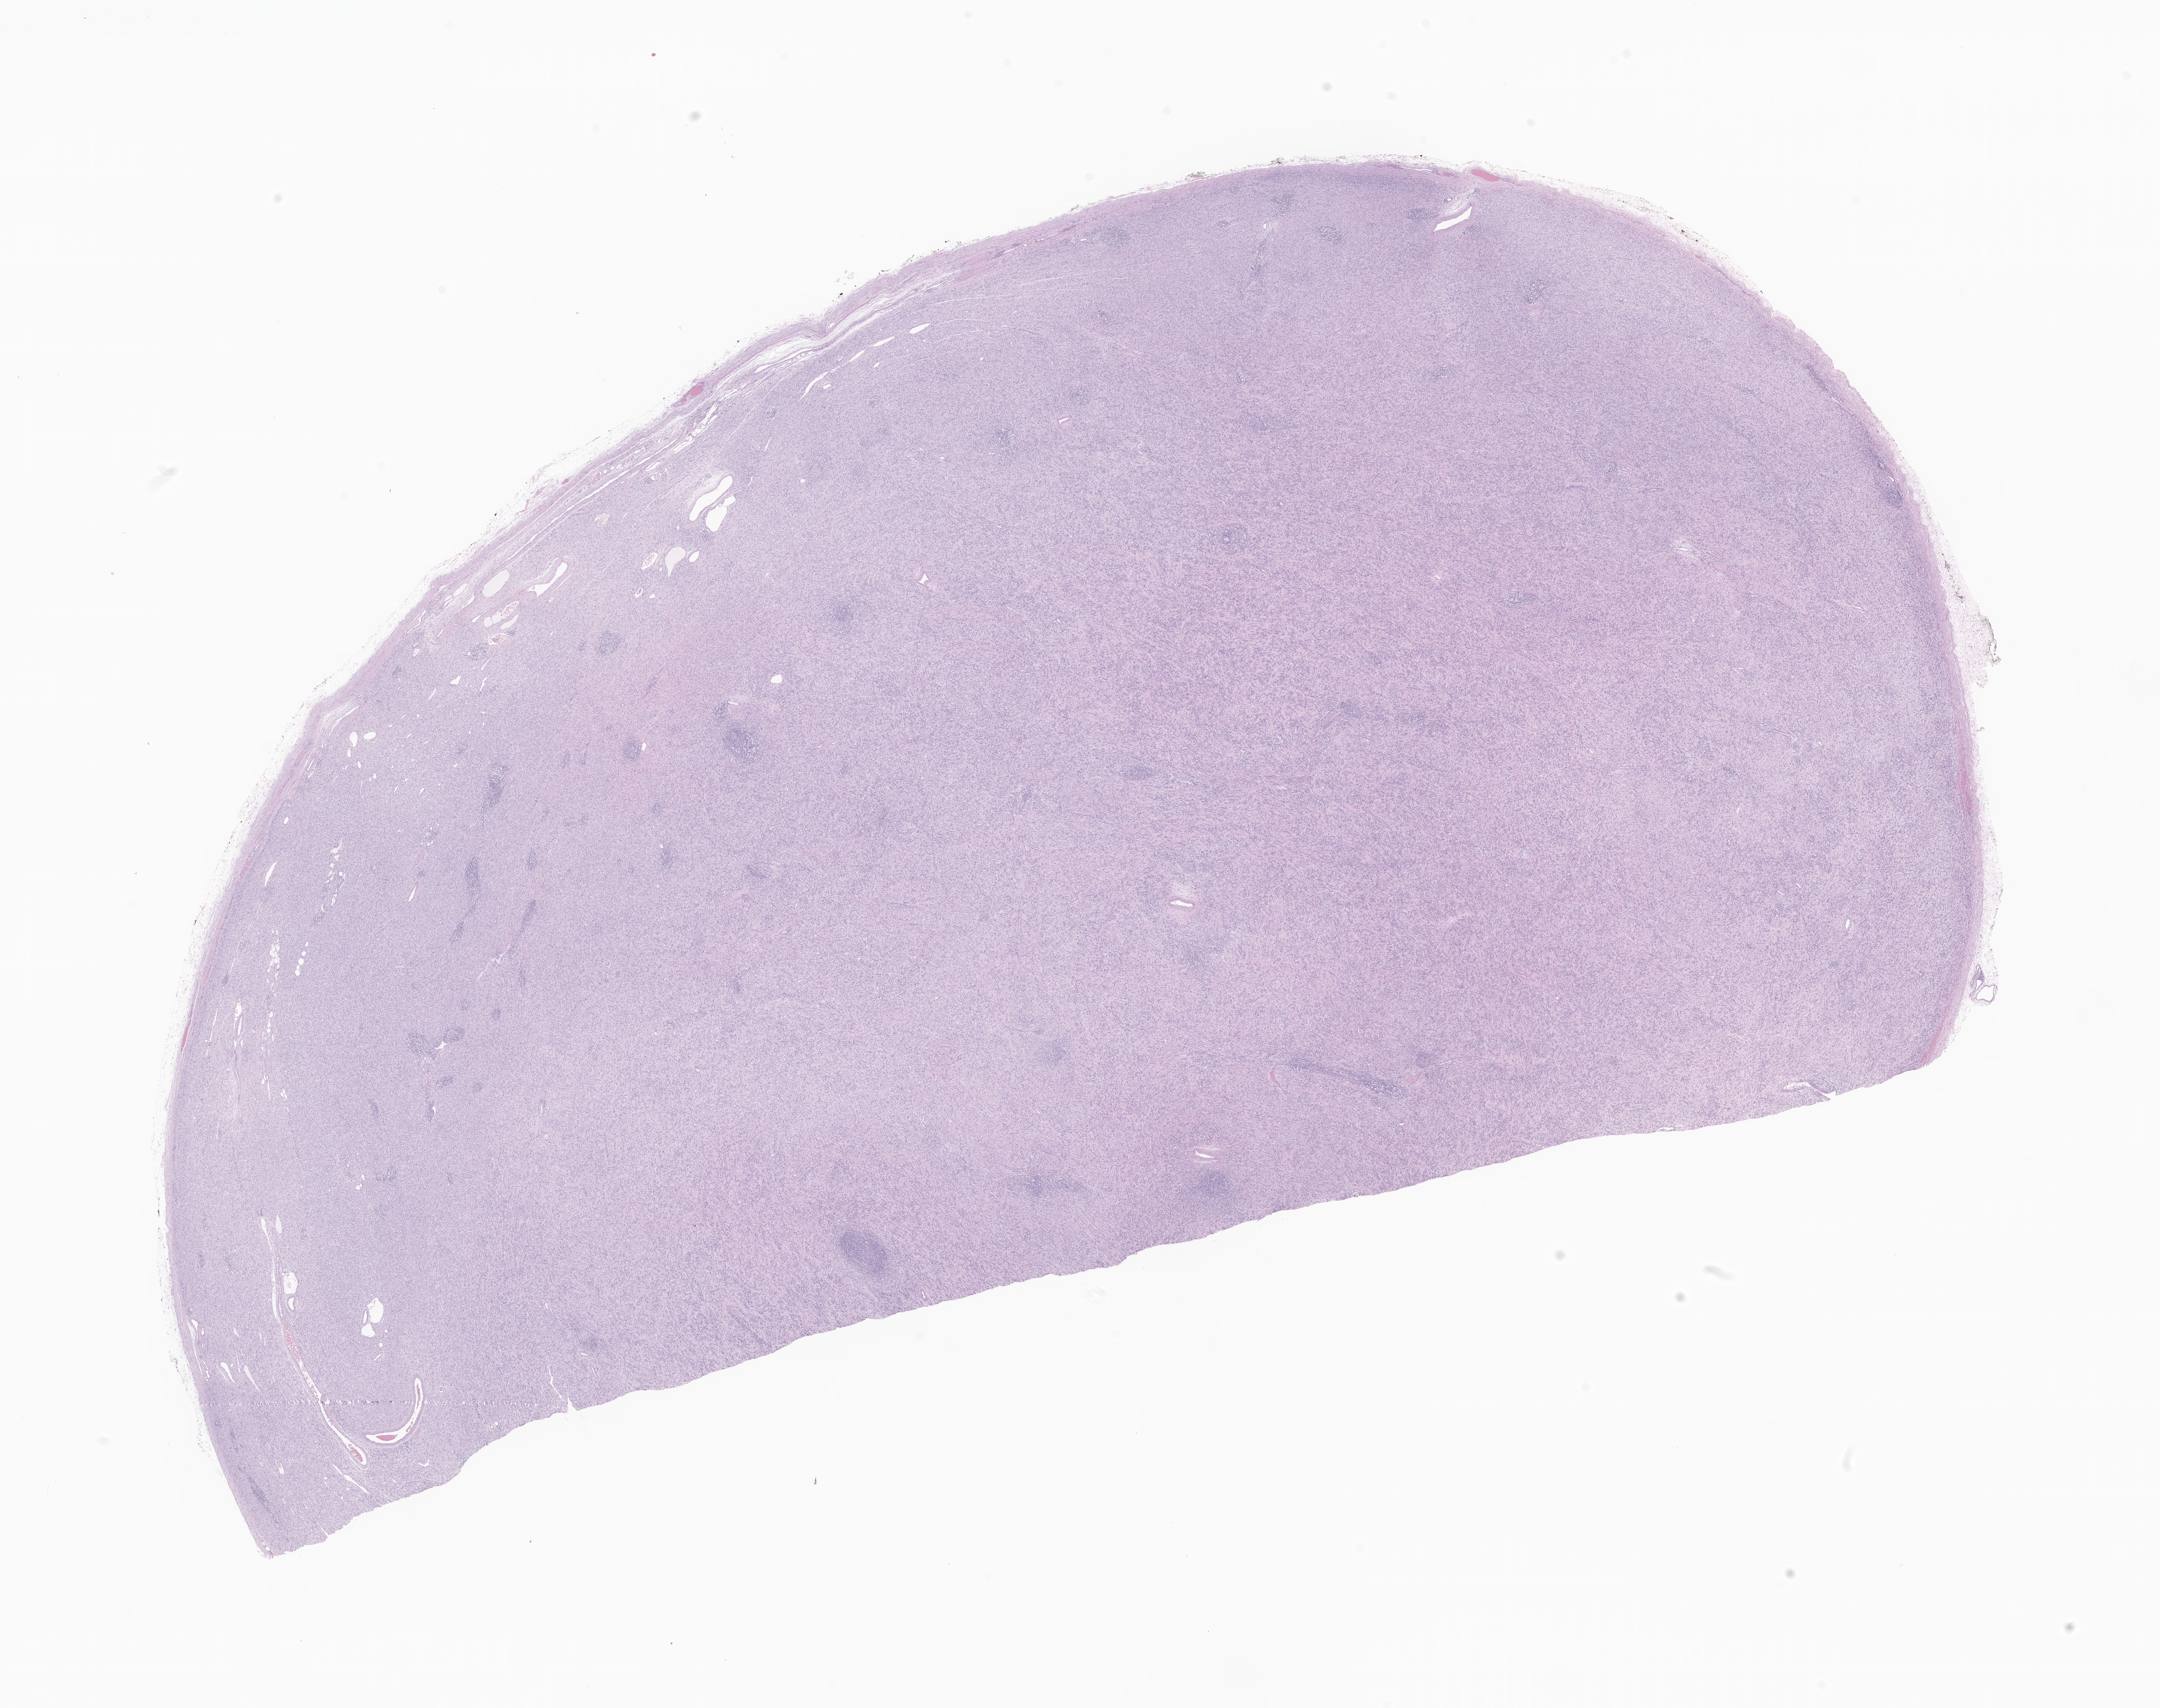
H&E whole-slide image of tumor tissue from the testis, shown as a low-resolution overview of the whole scanned area (about 26.2 x 20.7 mm); formalin-fixed paraffin-embedded section. Patient: male, age 52 months (4 years 4 months).
• diagnosis (ICD-O-3 morphology term): Spindle cell rhabdomyosarcoma